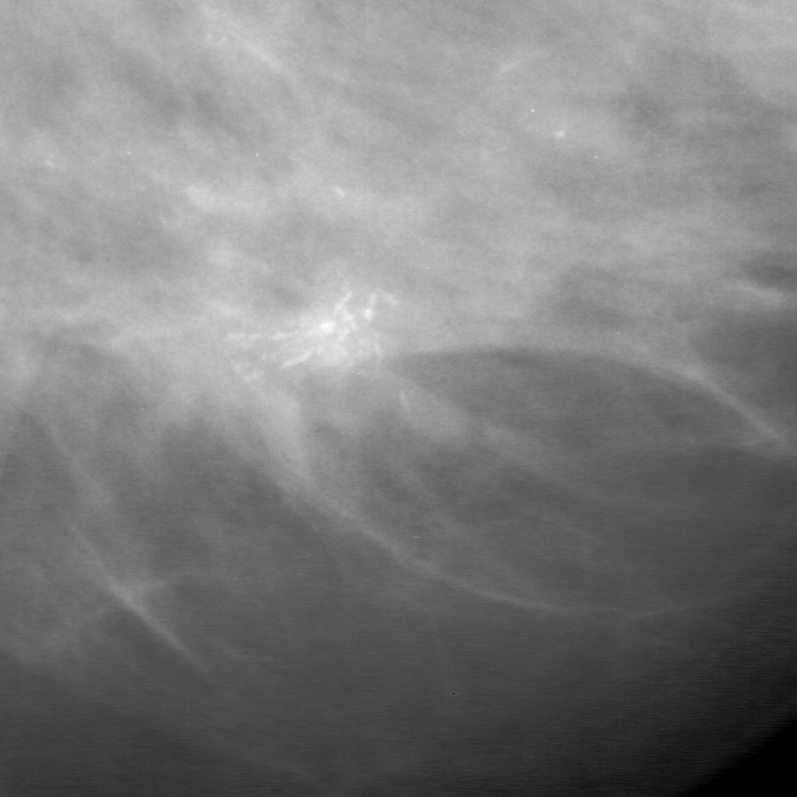
Cropped region of a digitized screen-film mammogram centred on a radiologist-marked abnormality, left breast, MLO view, BI-RADS breast density category 3 (scale 1–4).
- Finding: calcifications, morphology fine linear branching, distribution clustered; BI-RADS assessment category 5; subtlety rating 4 on a 1 (subtle) to 5 (obvious) scale; pathology (as recorded): malignant.